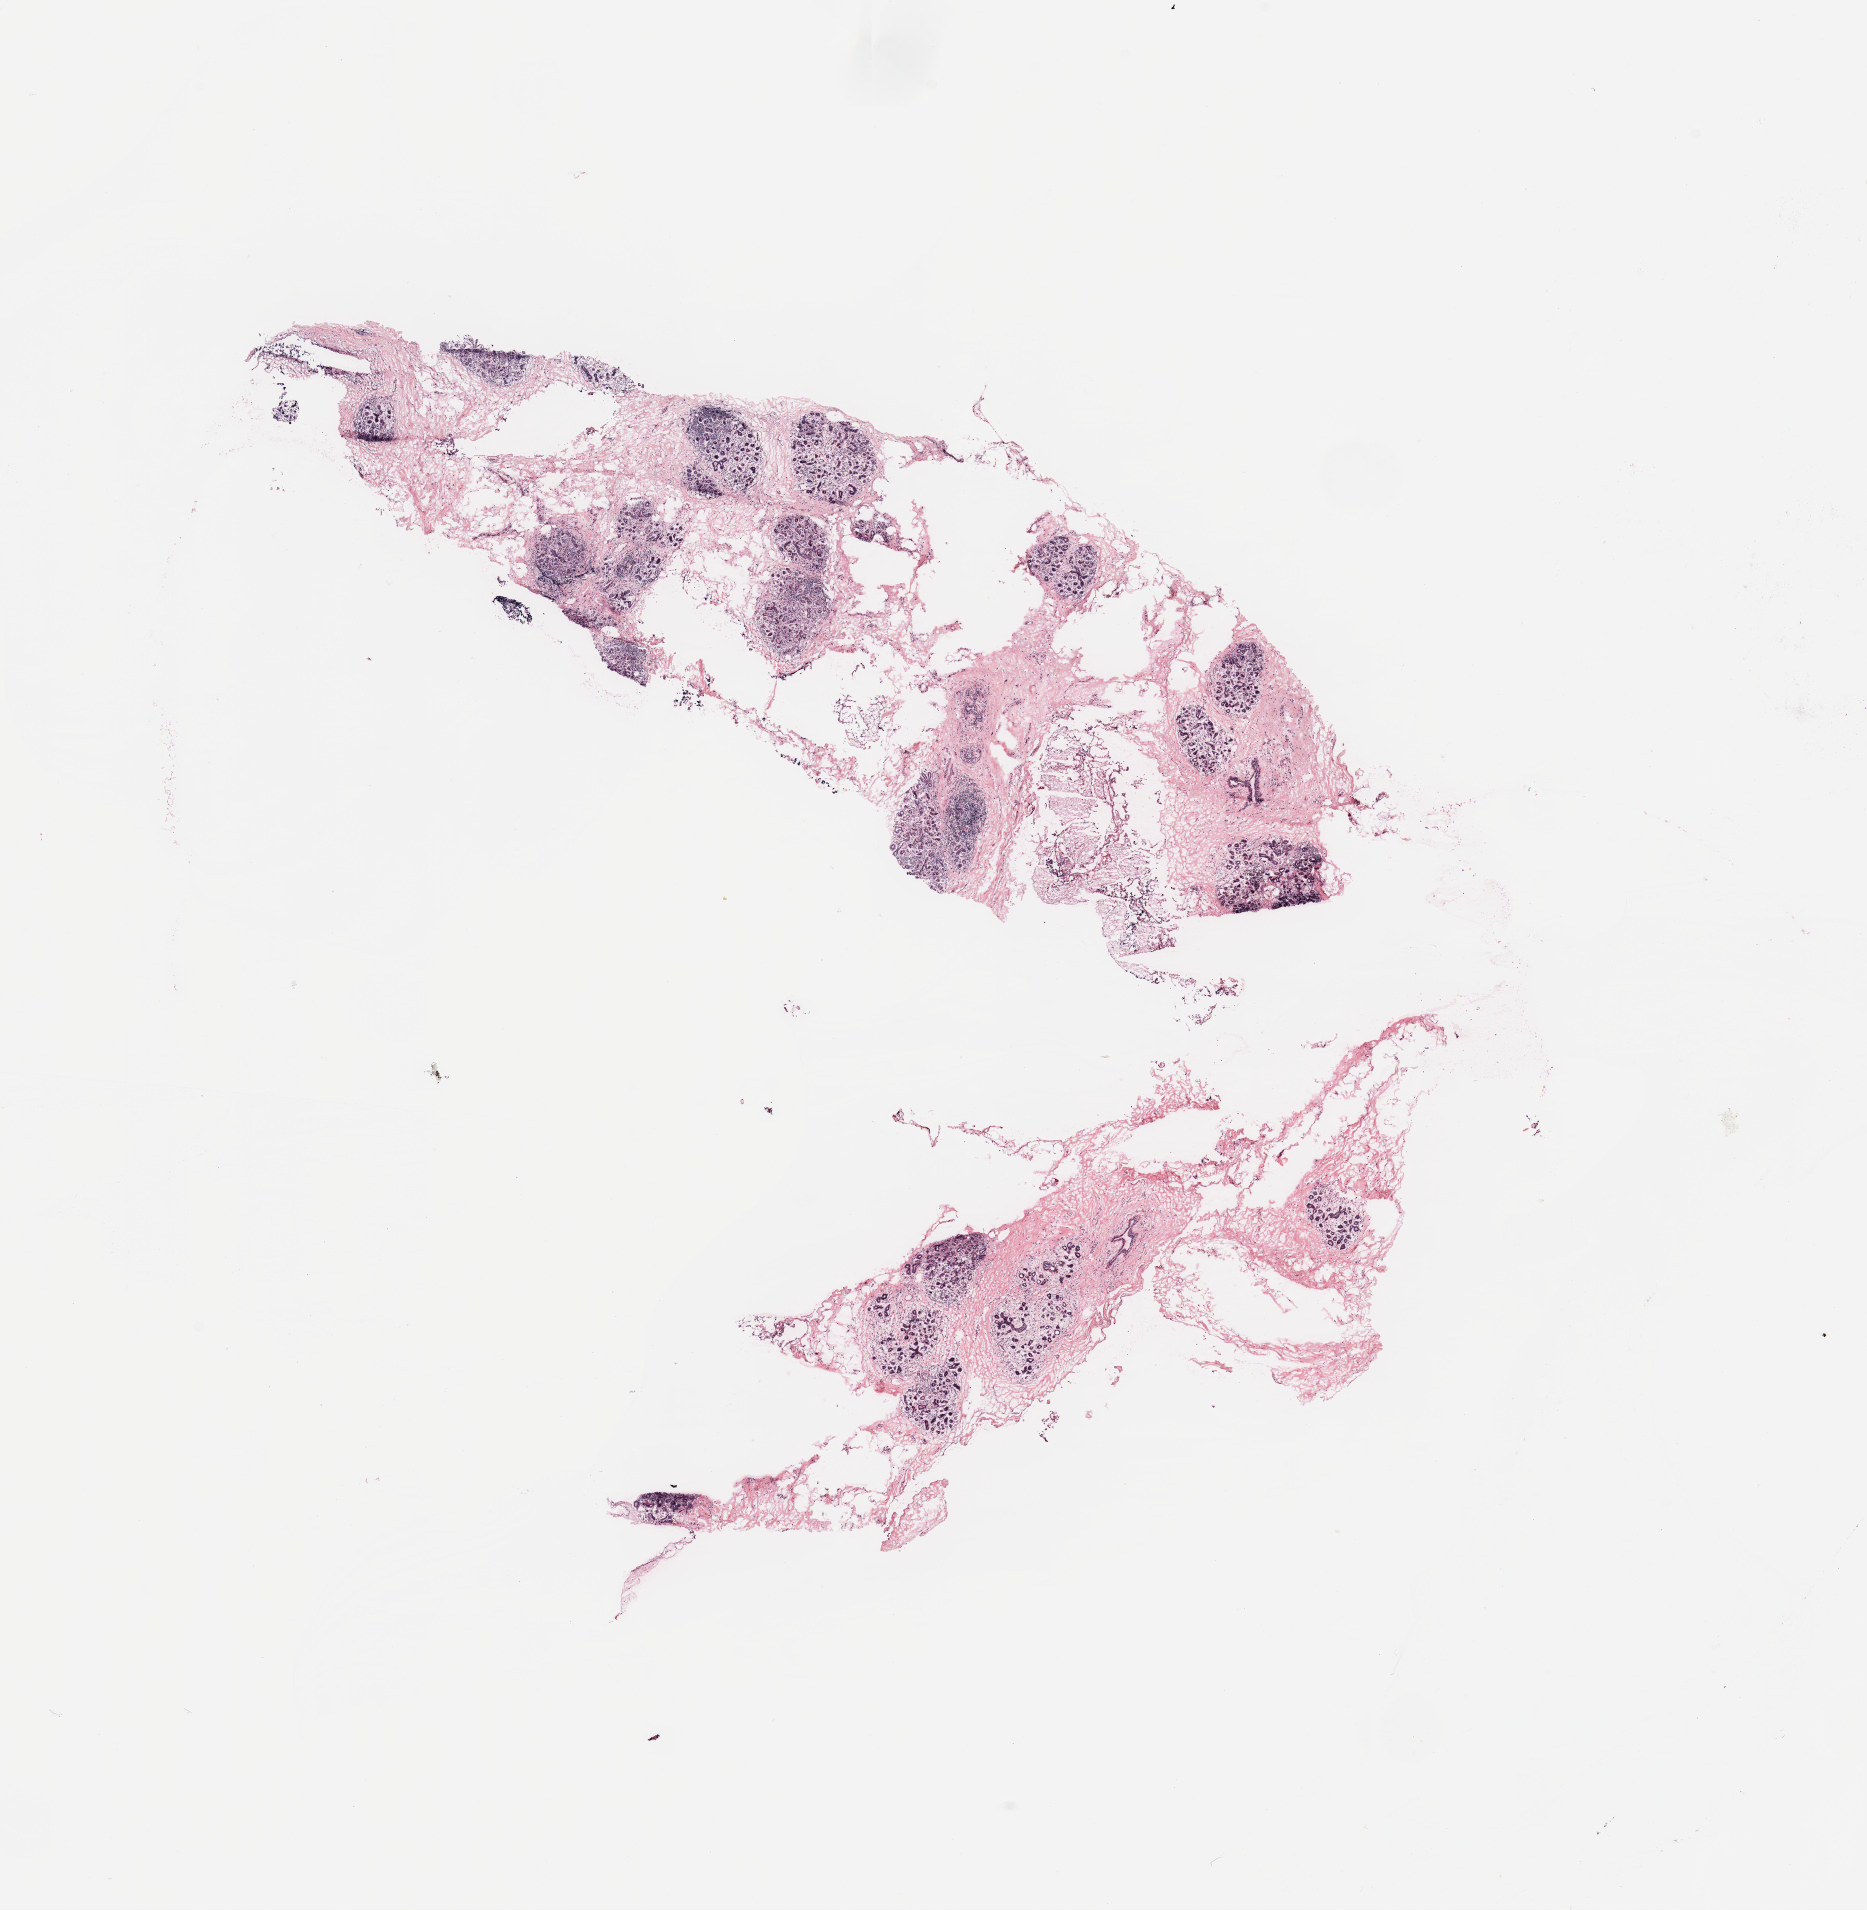
H&E-stained whole-slide image, low-resolution overview of the scanned area, about 14.8 x 15.1 mm (slide scanned at 20x), tumour tissue sample, breast. Patient: female, age 40 years.
Diagnosis: Infiltrating duct carcinoma, NOS.